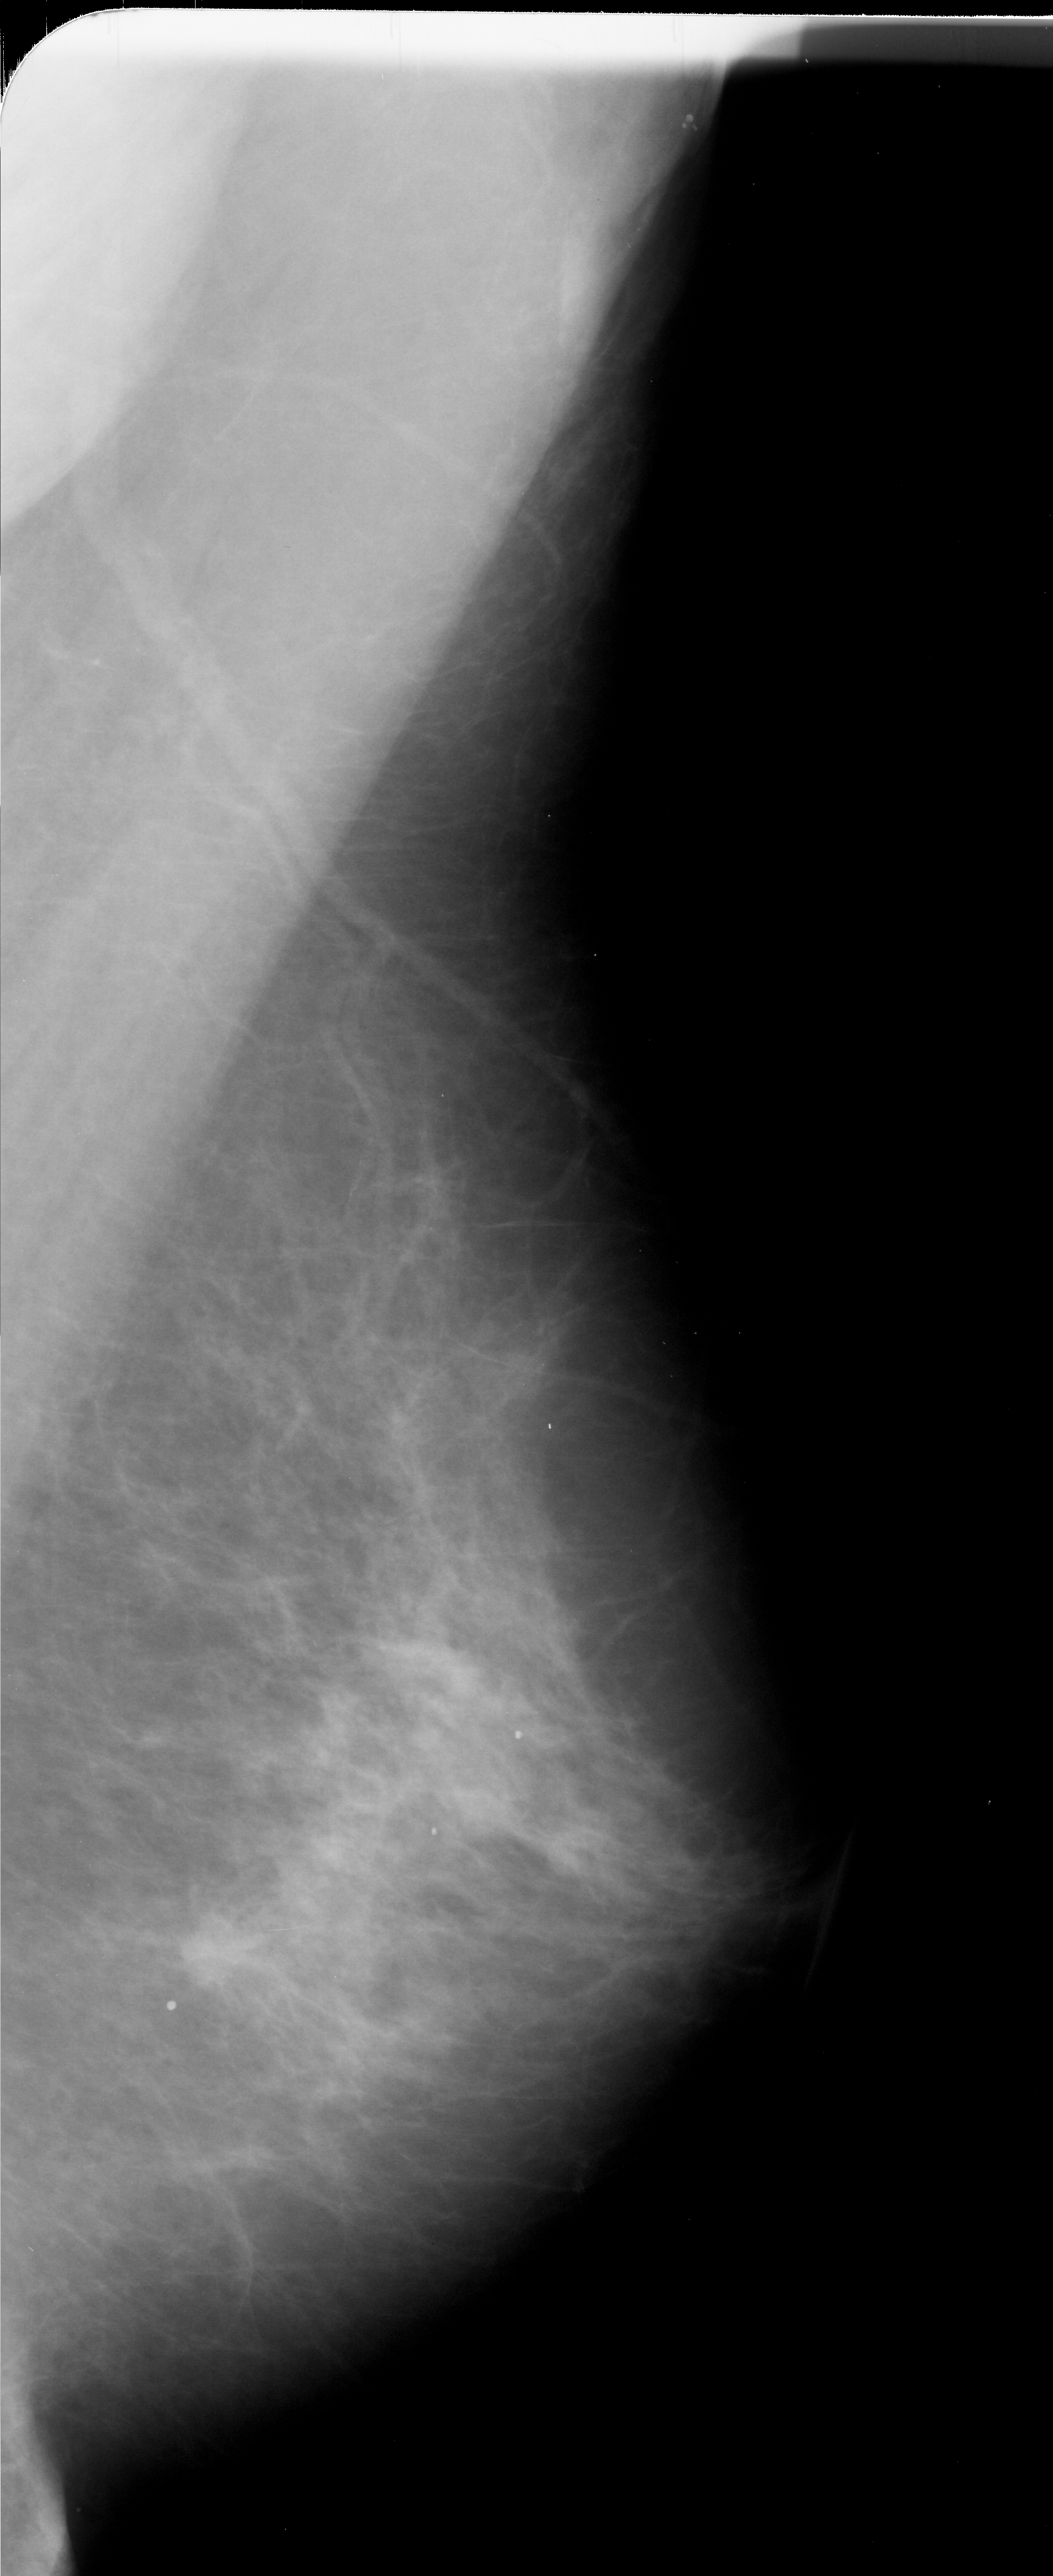
Digitized screen-film mammogram; right breast; mediolateral oblique (MLO) view; BI-RADS breast density category 3 (scale 1–4); 1053 × 2576 image matrix.
Expert-marked regions of interest on this image (one box per marked abnormality):
- mass, shape lobulated, margins ill defined; BI-RADS assessment category 4; subtlety rating 4 on a 1 (subtle) to 5 (obvious) scale; pathology (as recorded): malignant: bounding box <174,1912,247,1994> (left, top, right, bottom; pixels)